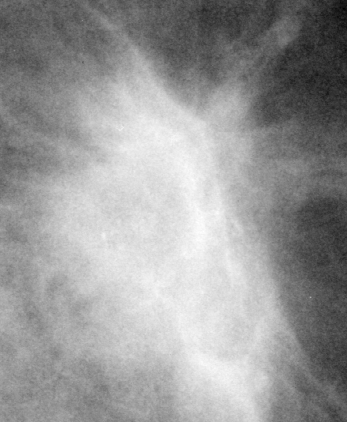
Cropped region of a digitized screen-film mammogram centred on a radiologist-marked abnormality, left breast, MLO view, BI-RADS breast density category 2 (scale 1–4).
Marked abnormality: mass, shape irregular / architectural distortion, margins spiculated; BI-RADS assessment category 5; subtlety rating 5 on a 1 (subtle) to 5 (obvious) scale; pathology result (as recorded, not read from the image): malignant.